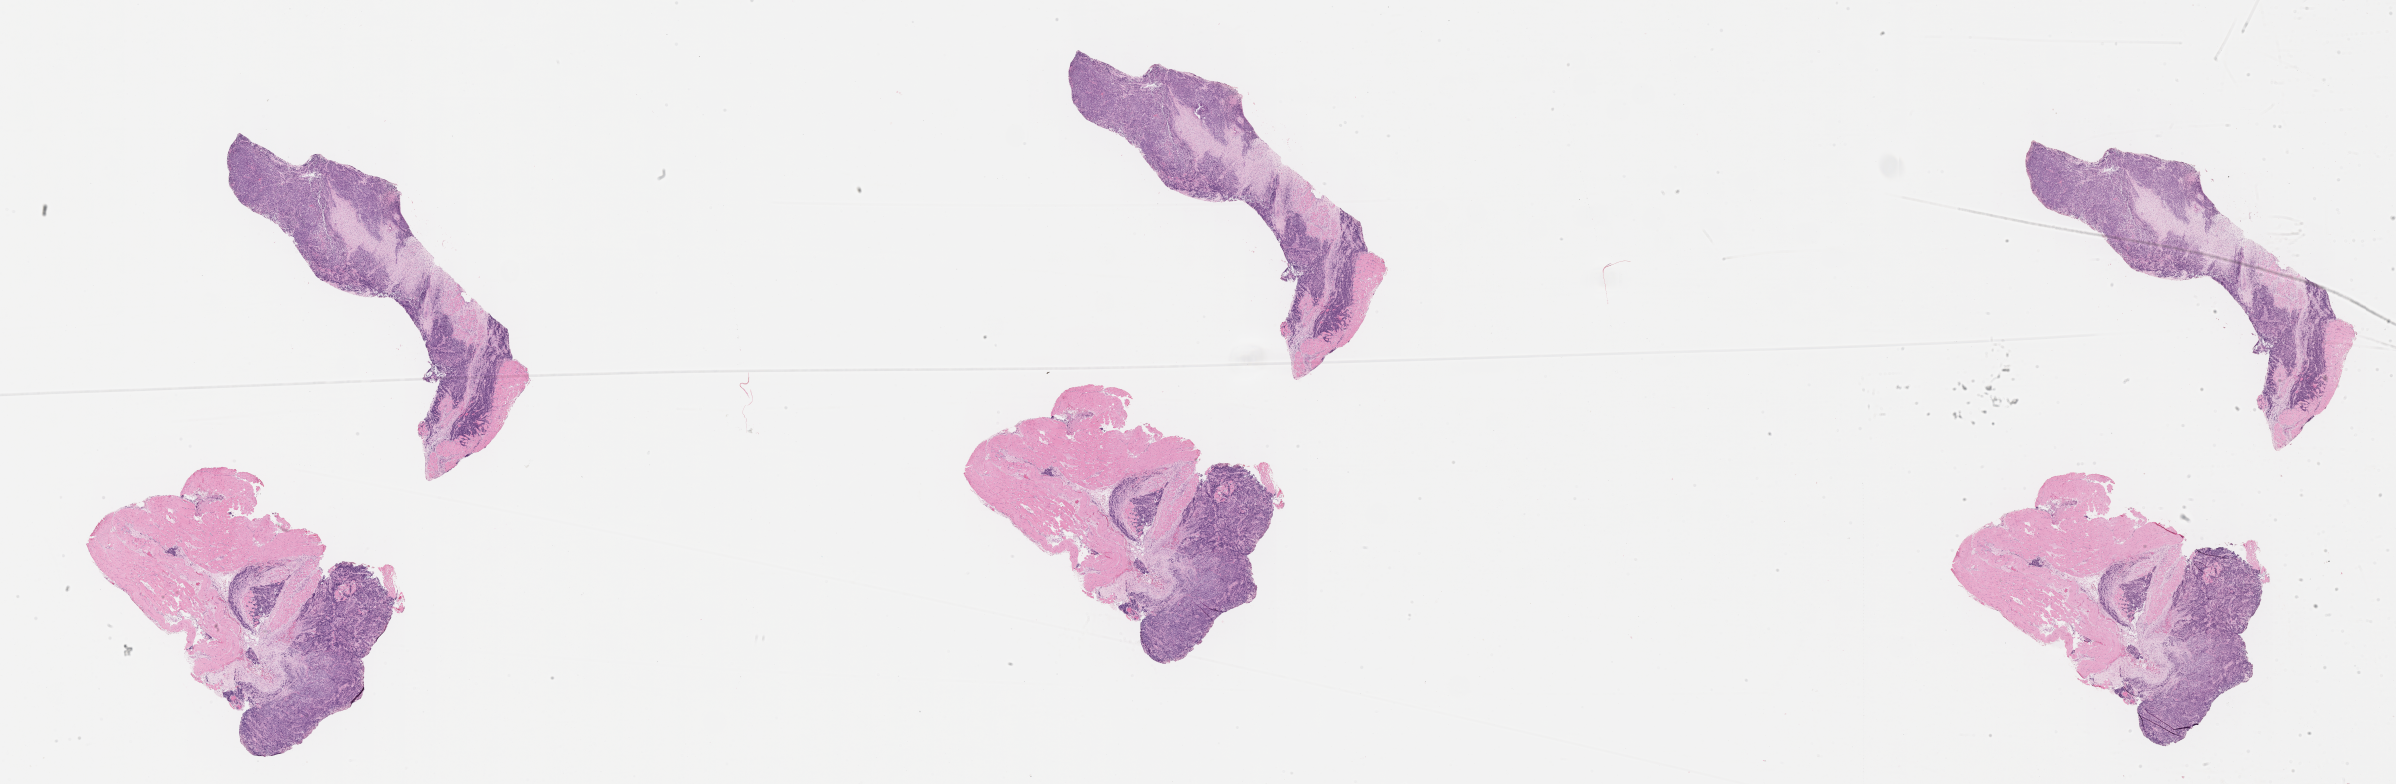
Haematoxylin and eosin whole-slide image of tumor tissue, shown as a low-resolution overview of the whole scanned area (about 38.7 x 12.7 mm); formalin-fixed paraffin-embedded section; site: soft tissue, forearm-right. Patient: female, age 1.2 years at diagnosis.
Stage (as recorded): 3. Metastatic status at presentation (as recorded): non-metastatic. Diagnosis: rhabdomyosarcoma; histological classification: embryonal rhabdomyosarcoma.